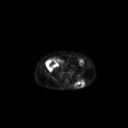
FDG PET of an extremity soft-tissue mass (from a PET/CT study), one axial slice. Position 89 of 267 along the scan axis. 3.27 mm slice thickness. 128 × 128 image matrix, field of view 700 × 700 mm. Male patient, age 69 years. Case-level facts recorded for this patient, not image findings: histological type: leiomyosarcoma; grade: intermediate; site of the primary tumour: left pelvis.
Structures marked on this image (expert contour drawn on MRI and transferred to this co-registered scan by the dataset authors):
- gross tumour volume (mass): box from (x=74, y=79) to (x=86, y=88) px